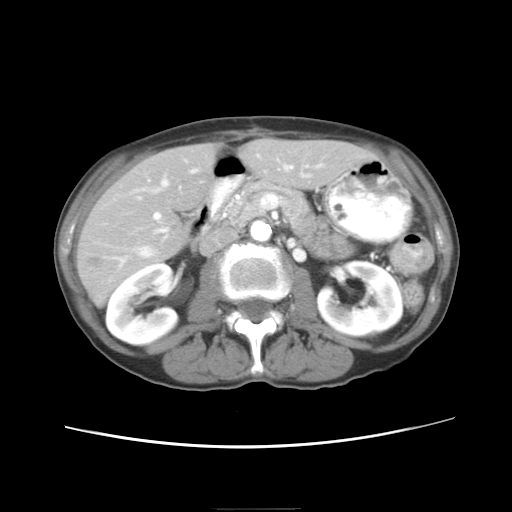
Contrast-enhanced abdominal CT, one axial slice; slice 9 of 26 in the series (ordered by position); reconstruction kernel STANDARD; 120 kVp; intravenous contrast given; soft-tissue window (W 400 / L 40 HU); 7.5 mm slice thickness; 512 × 512 image matrix, field of view 340 × 340 mm. Female patient, age 65 years. From the clinical record (not read from this slice): diagnosis: colorectal cancer liver metastases, imaged before liver resection.
Annotated regions visible in this slice (expert manual segmentation):
- hepatic veins: bounding box (x1, y1, x2, y2) in pixels: (133, 159, 309, 267)
- liver: (77, 140, 367, 303)
- planned liver remnant (the part of the liver to remain after resection): (79, 140, 367, 303)
- portal vein (with intrahepatic branches): (148, 165, 292, 232)
- liver metastasis: (90, 259, 97, 266)